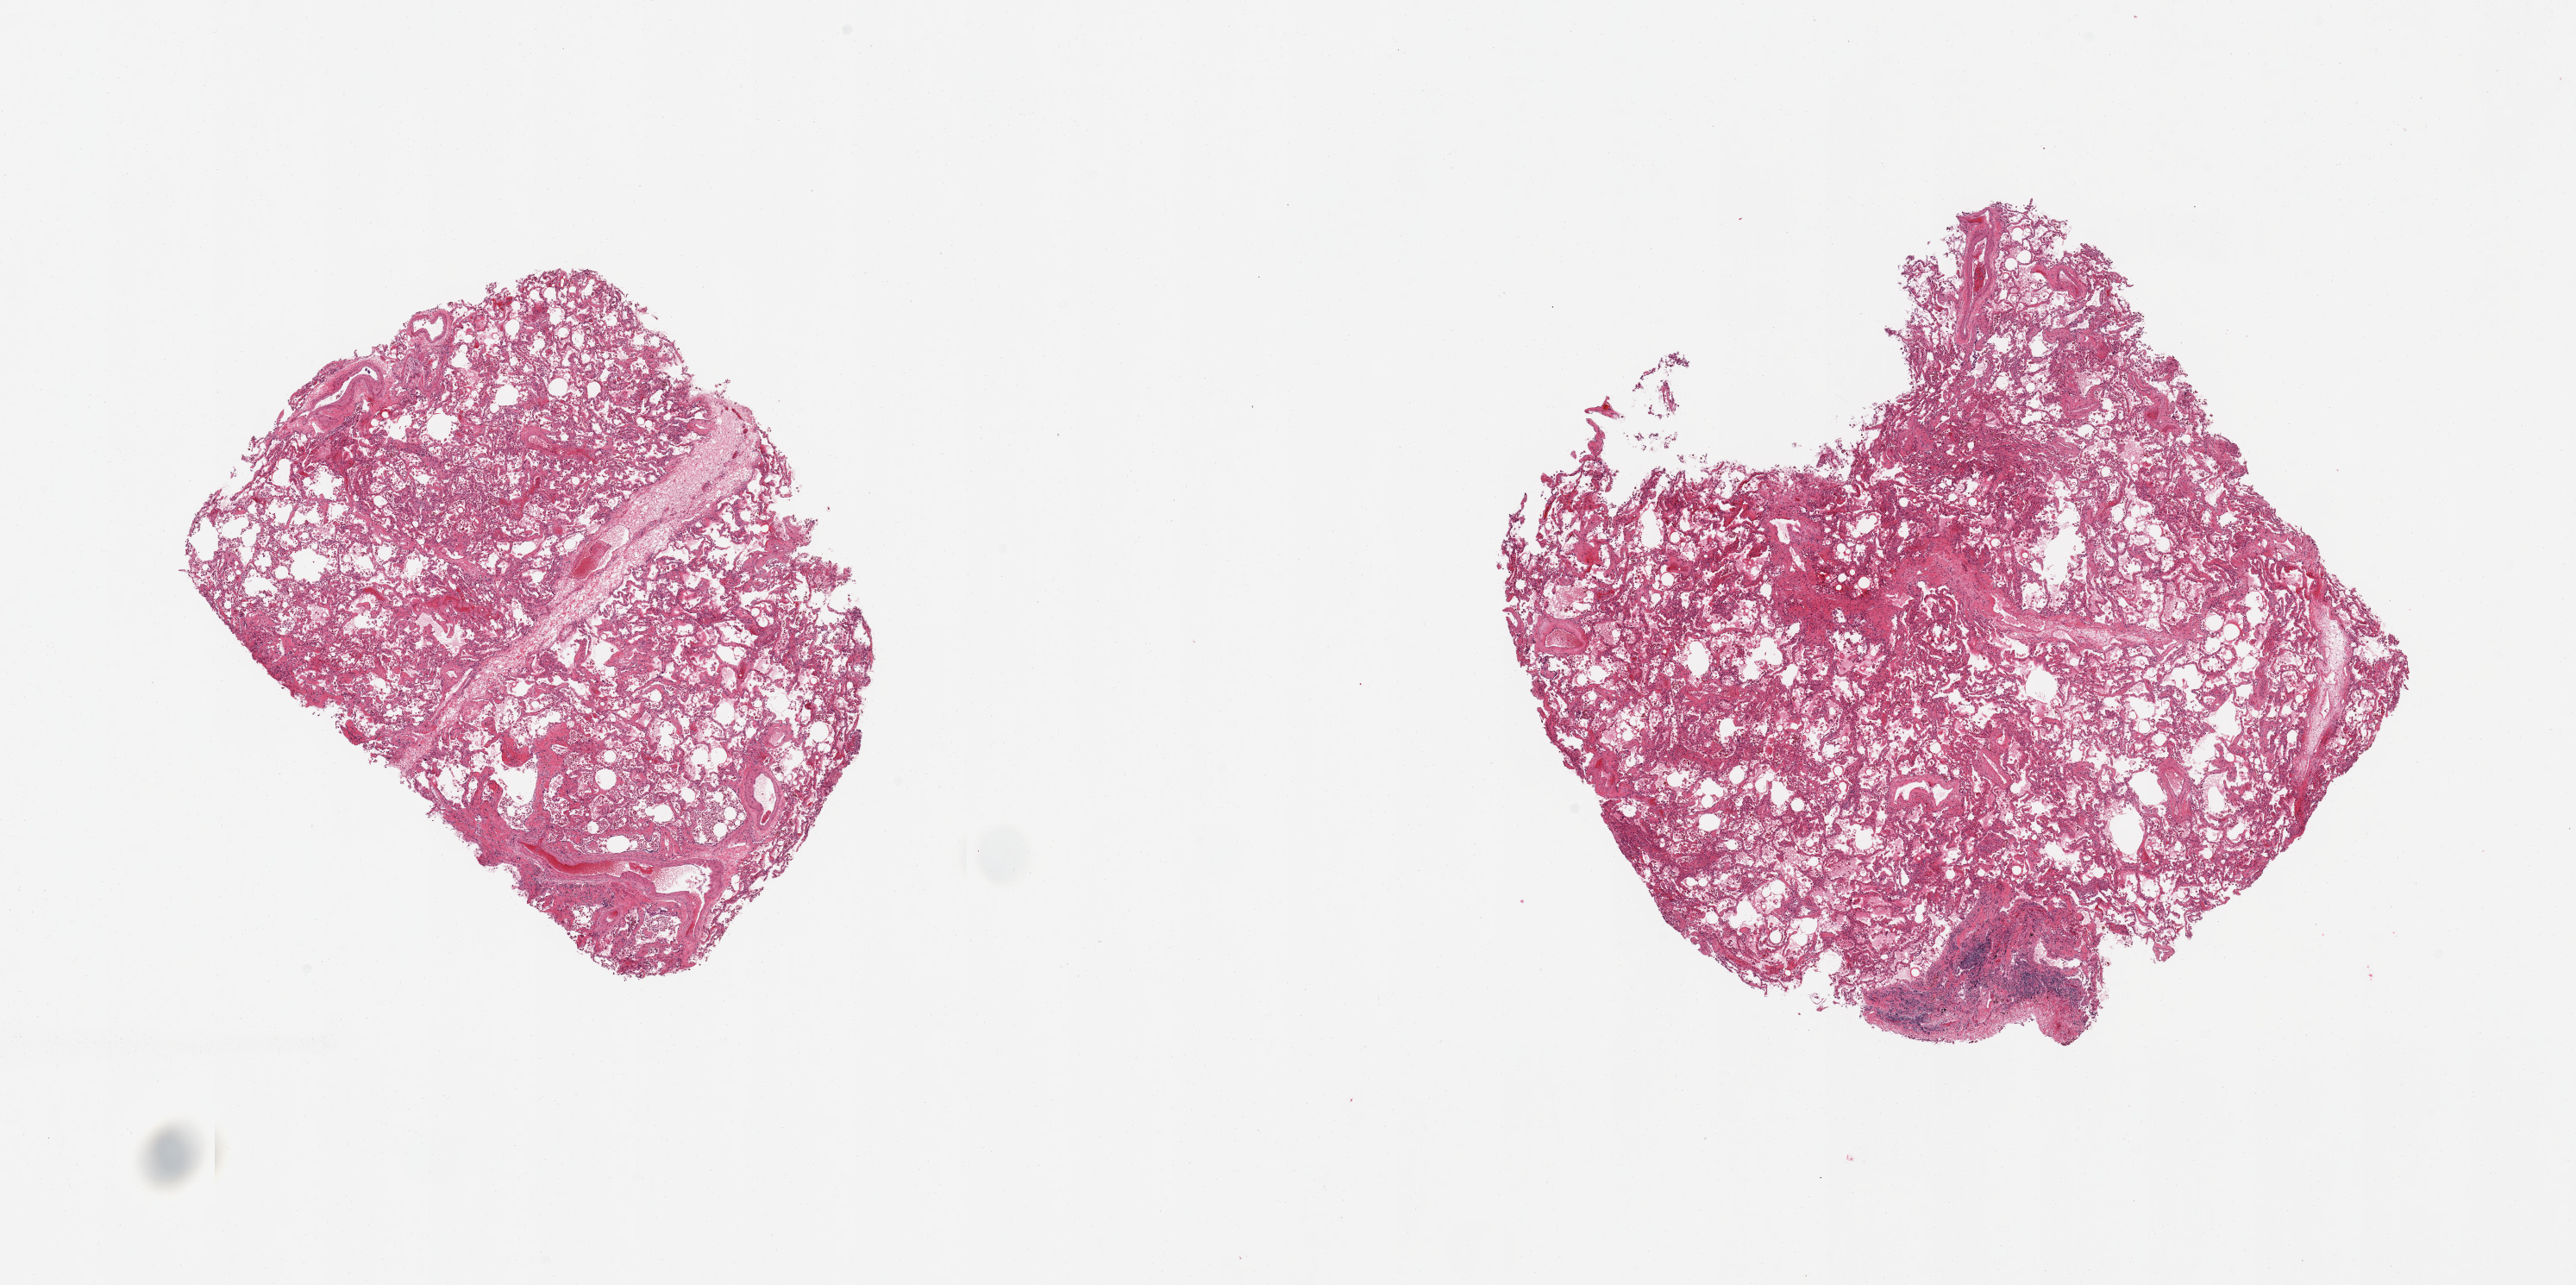
Whole-slide image, H&E stain, brightfield, low-resolution overview of the scanned area, about 23.6 x 11.8 mm (acquisition: 20x scan); PAXgene-fixed, paraffin-embedded tissue; section of lung (target tissue); tissue donor sample.
* pathologist's review note for this sample: 2 pieces, patchy mild congestion, focal chronic pneumonitis